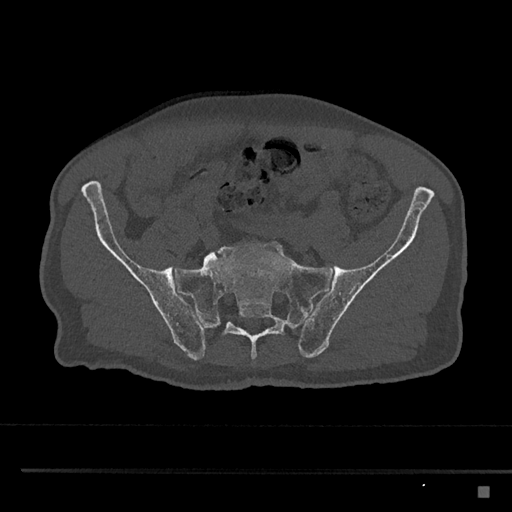
CT including the spine, one axial slice. Slice 514 of 797 in the series (ordered by position). 120 kVp. Bone window (W 1800 / L 400 HU). 0.5 mm slice thickness. 512 × 512 image matrix. Patient: male, 59 years. Case-level facts recorded for this patient, not image findings: primary cancer: prostate.
Outlined on this slice (semi-automatic segmentation, software-assisted and operator-edited):
- L5 vertebra: box from (x=205, y=255) to (x=210, y=259) px